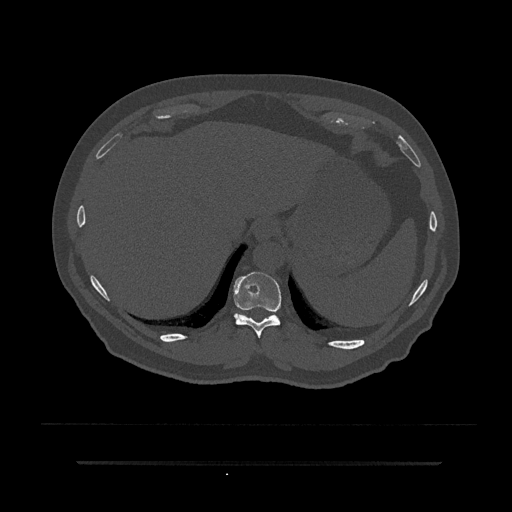
CT including the spine, one axial slice. Slice 319 of 797 in the series (ordered by position). Bone window (W 1800 / L 400 HU). 0.5 mm slice thickness. 512 × 512 image matrix. Male patient, age 59 years. Case-level facts recorded for this patient, not image findings: primary cancer: bile ducts; vertebrae with lytic lesions (as recorded): T10.
Outlined on this slice (semi-automatically segmented with operator editing):
- T10 vertebra: box from (x=233, y=272) to (x=281, y=338) px
- T11 vertebra: (x=236, y=313)–(x=247, y=317)